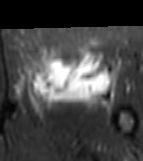
MRI of an extremity soft-tissue mass, one axial slice. Slice 37 of 81 in the series (ordered by position). STIR. MR volume resampled by the dataset authors to the PET/CT grid (not the native acquisition matrix). 3.27 mm slice thickness. 143 × 161 image matrix, field of view 140 × 157 mm. Female patient. Case-level facts recorded for this patient, not image findings: histological type: myxofibrosarcoma; grade: intermediate; site of the primary tumour: left thigh.
Structures marked on this image (expert contour drawn on MRI and transferred to this co-registered scan by the dataset authors):
- gross tumour volume including surrounding oedema: box from (x=26, y=47) to (x=118, y=114) px
- gross tumour volume (mass): (x=31, y=47)–(x=109, y=100)